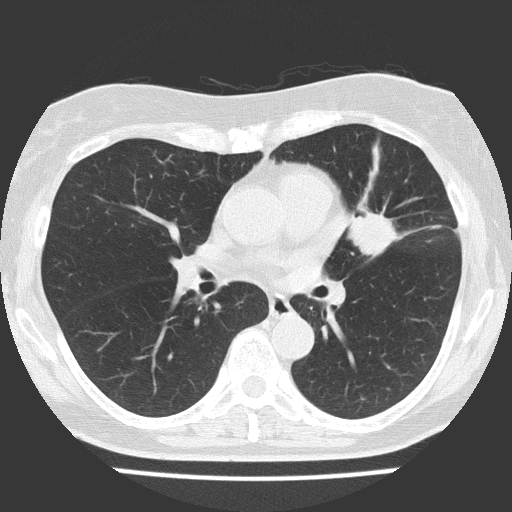
Low-dose screening chest CT, one axial slice; position 80 of 151 along the scan axis; reconstruction kernel FC51; 120 kVp; lung window (W 1500 / L -600 HU); 512 × 512 image matrix, field of view 309 × 309 mm.
Outlined on this slice (outlined manually by an expert reader):
- lesion 1 (tumor, upper lobe of left lung): bounding box (x1, y1, x2, y2) in pixels: (348, 211, 400, 257)